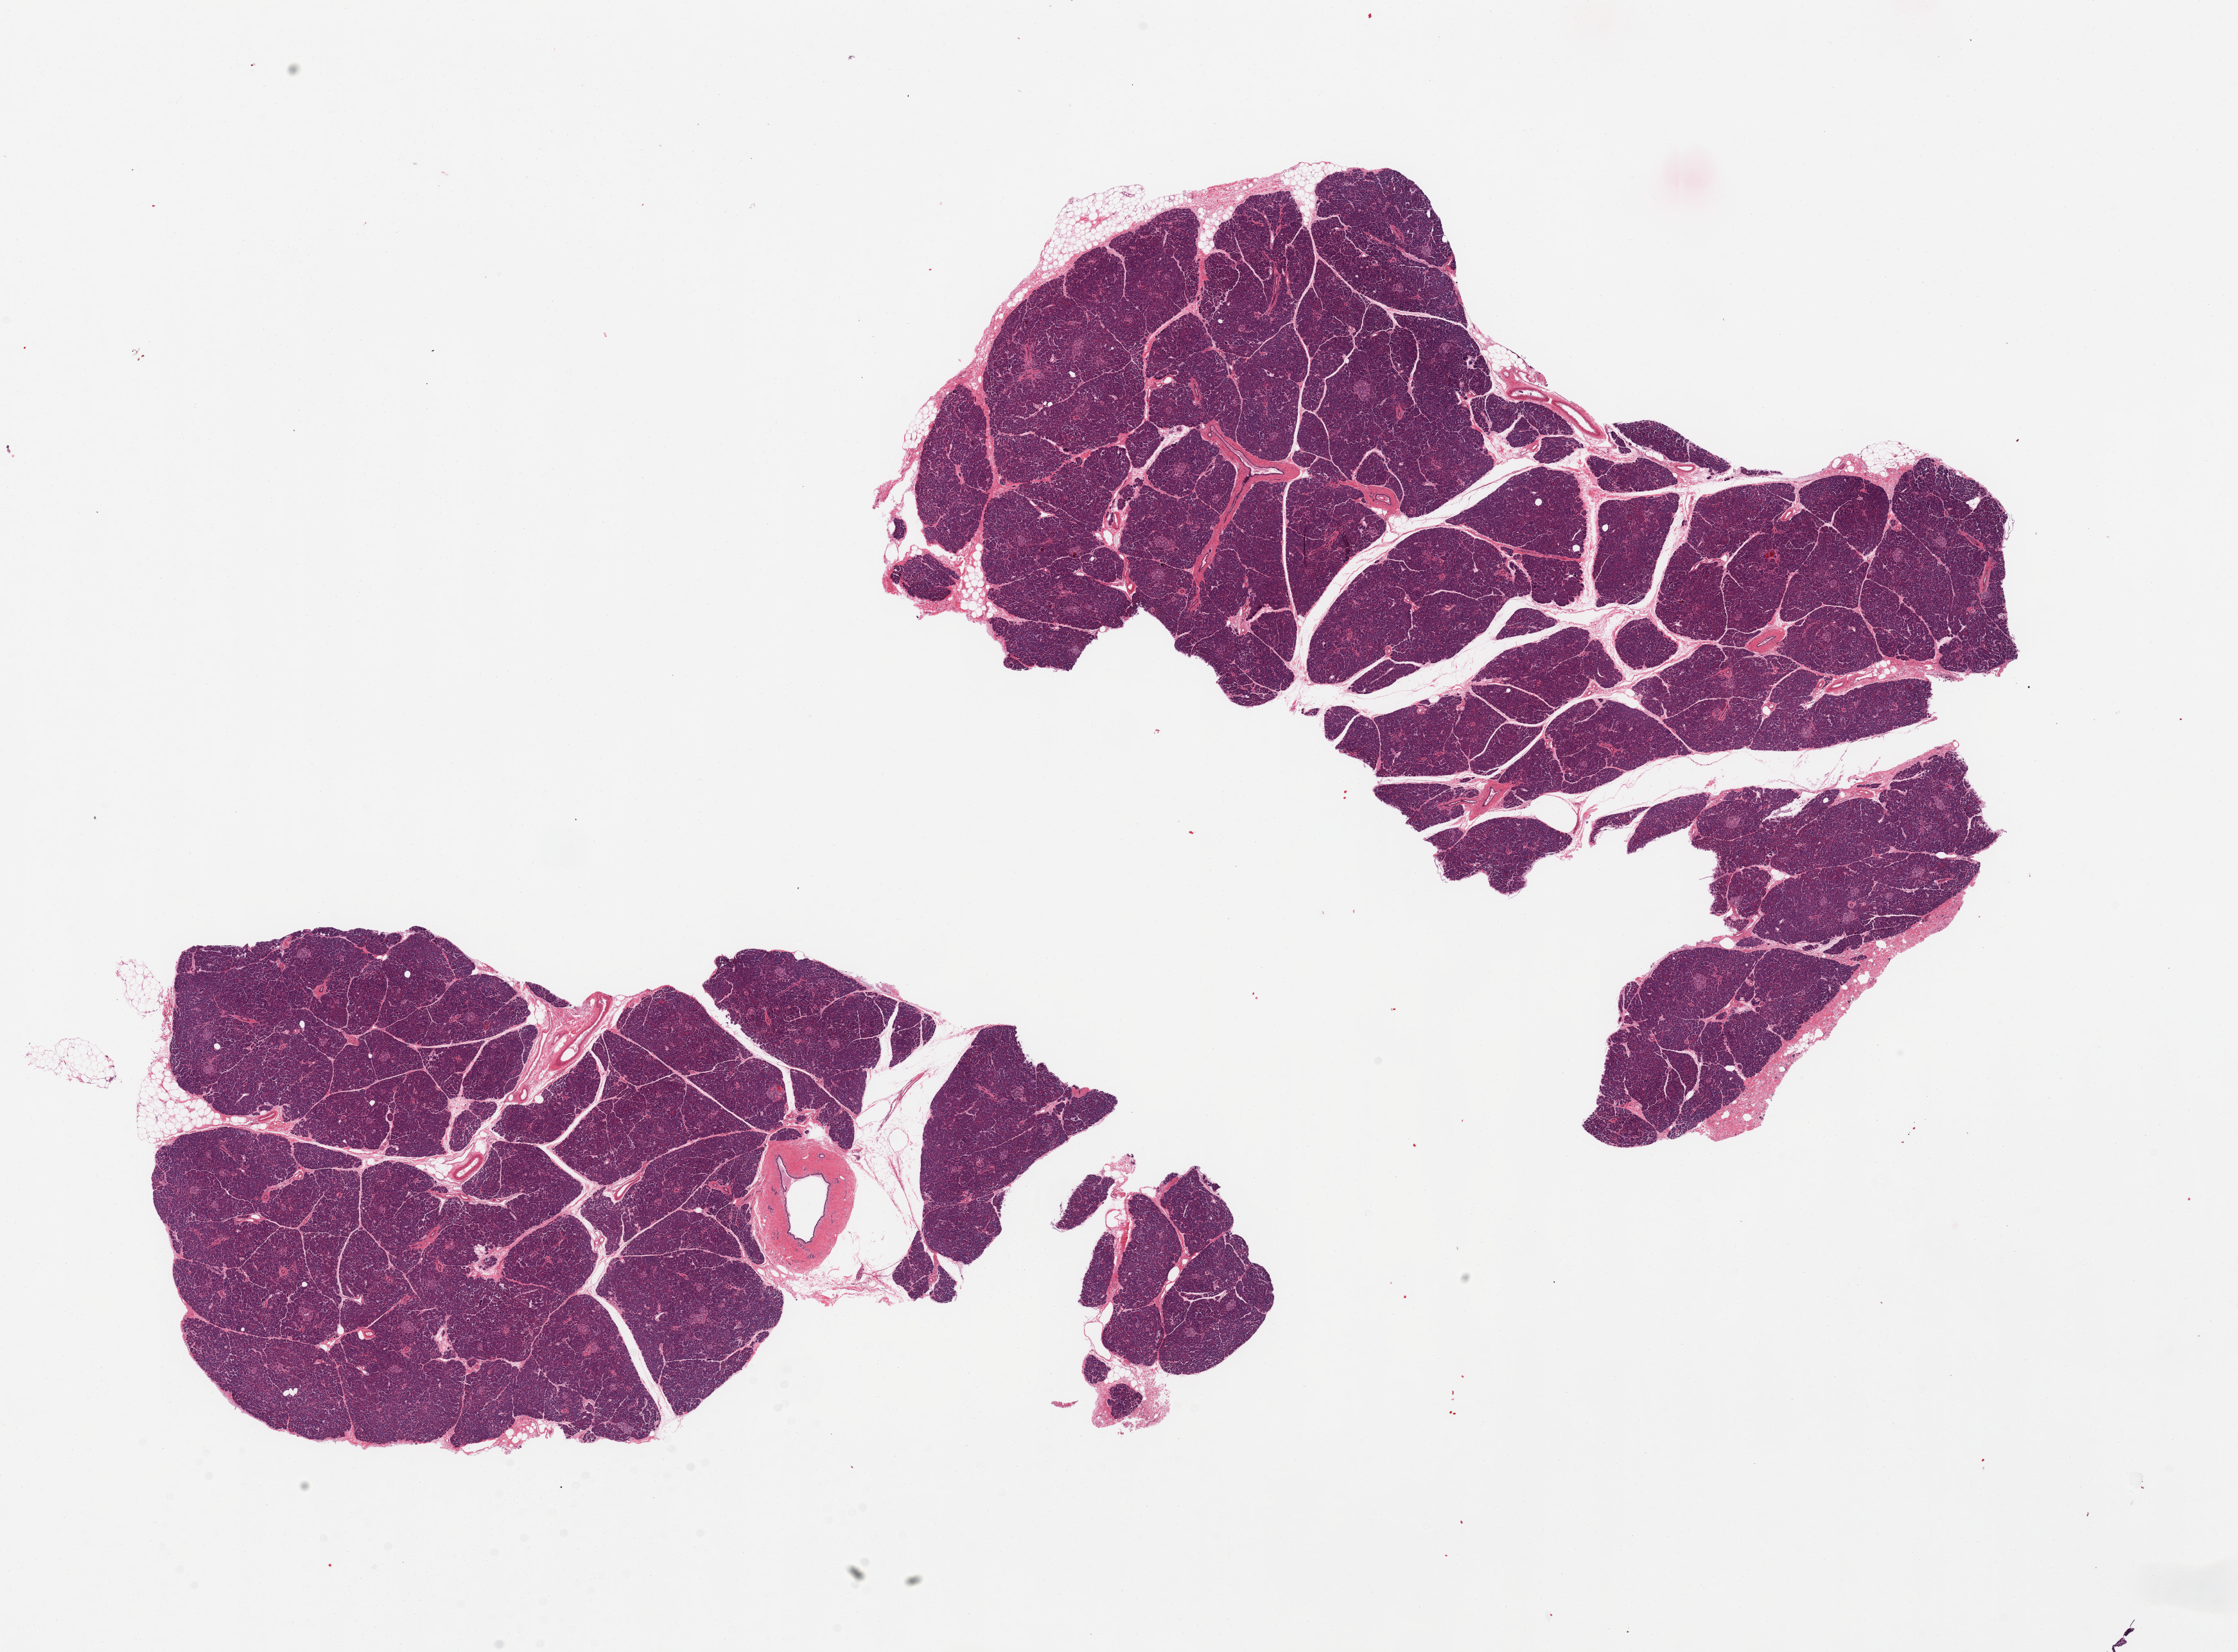
Whole-slide image, hematoxylin and eosin (H&E) stain — whole scanned area (about 27.6 x 20.4 mm, acquisition: 20x scan) shown as a low-resolution overview, PAXgene-fixed, paraffin-embedded tissue, sampled site (target tissue): pancreas, tissue donor sample.
* review note (as recorded): 2 pieces, well- preserved; Islets well visualized